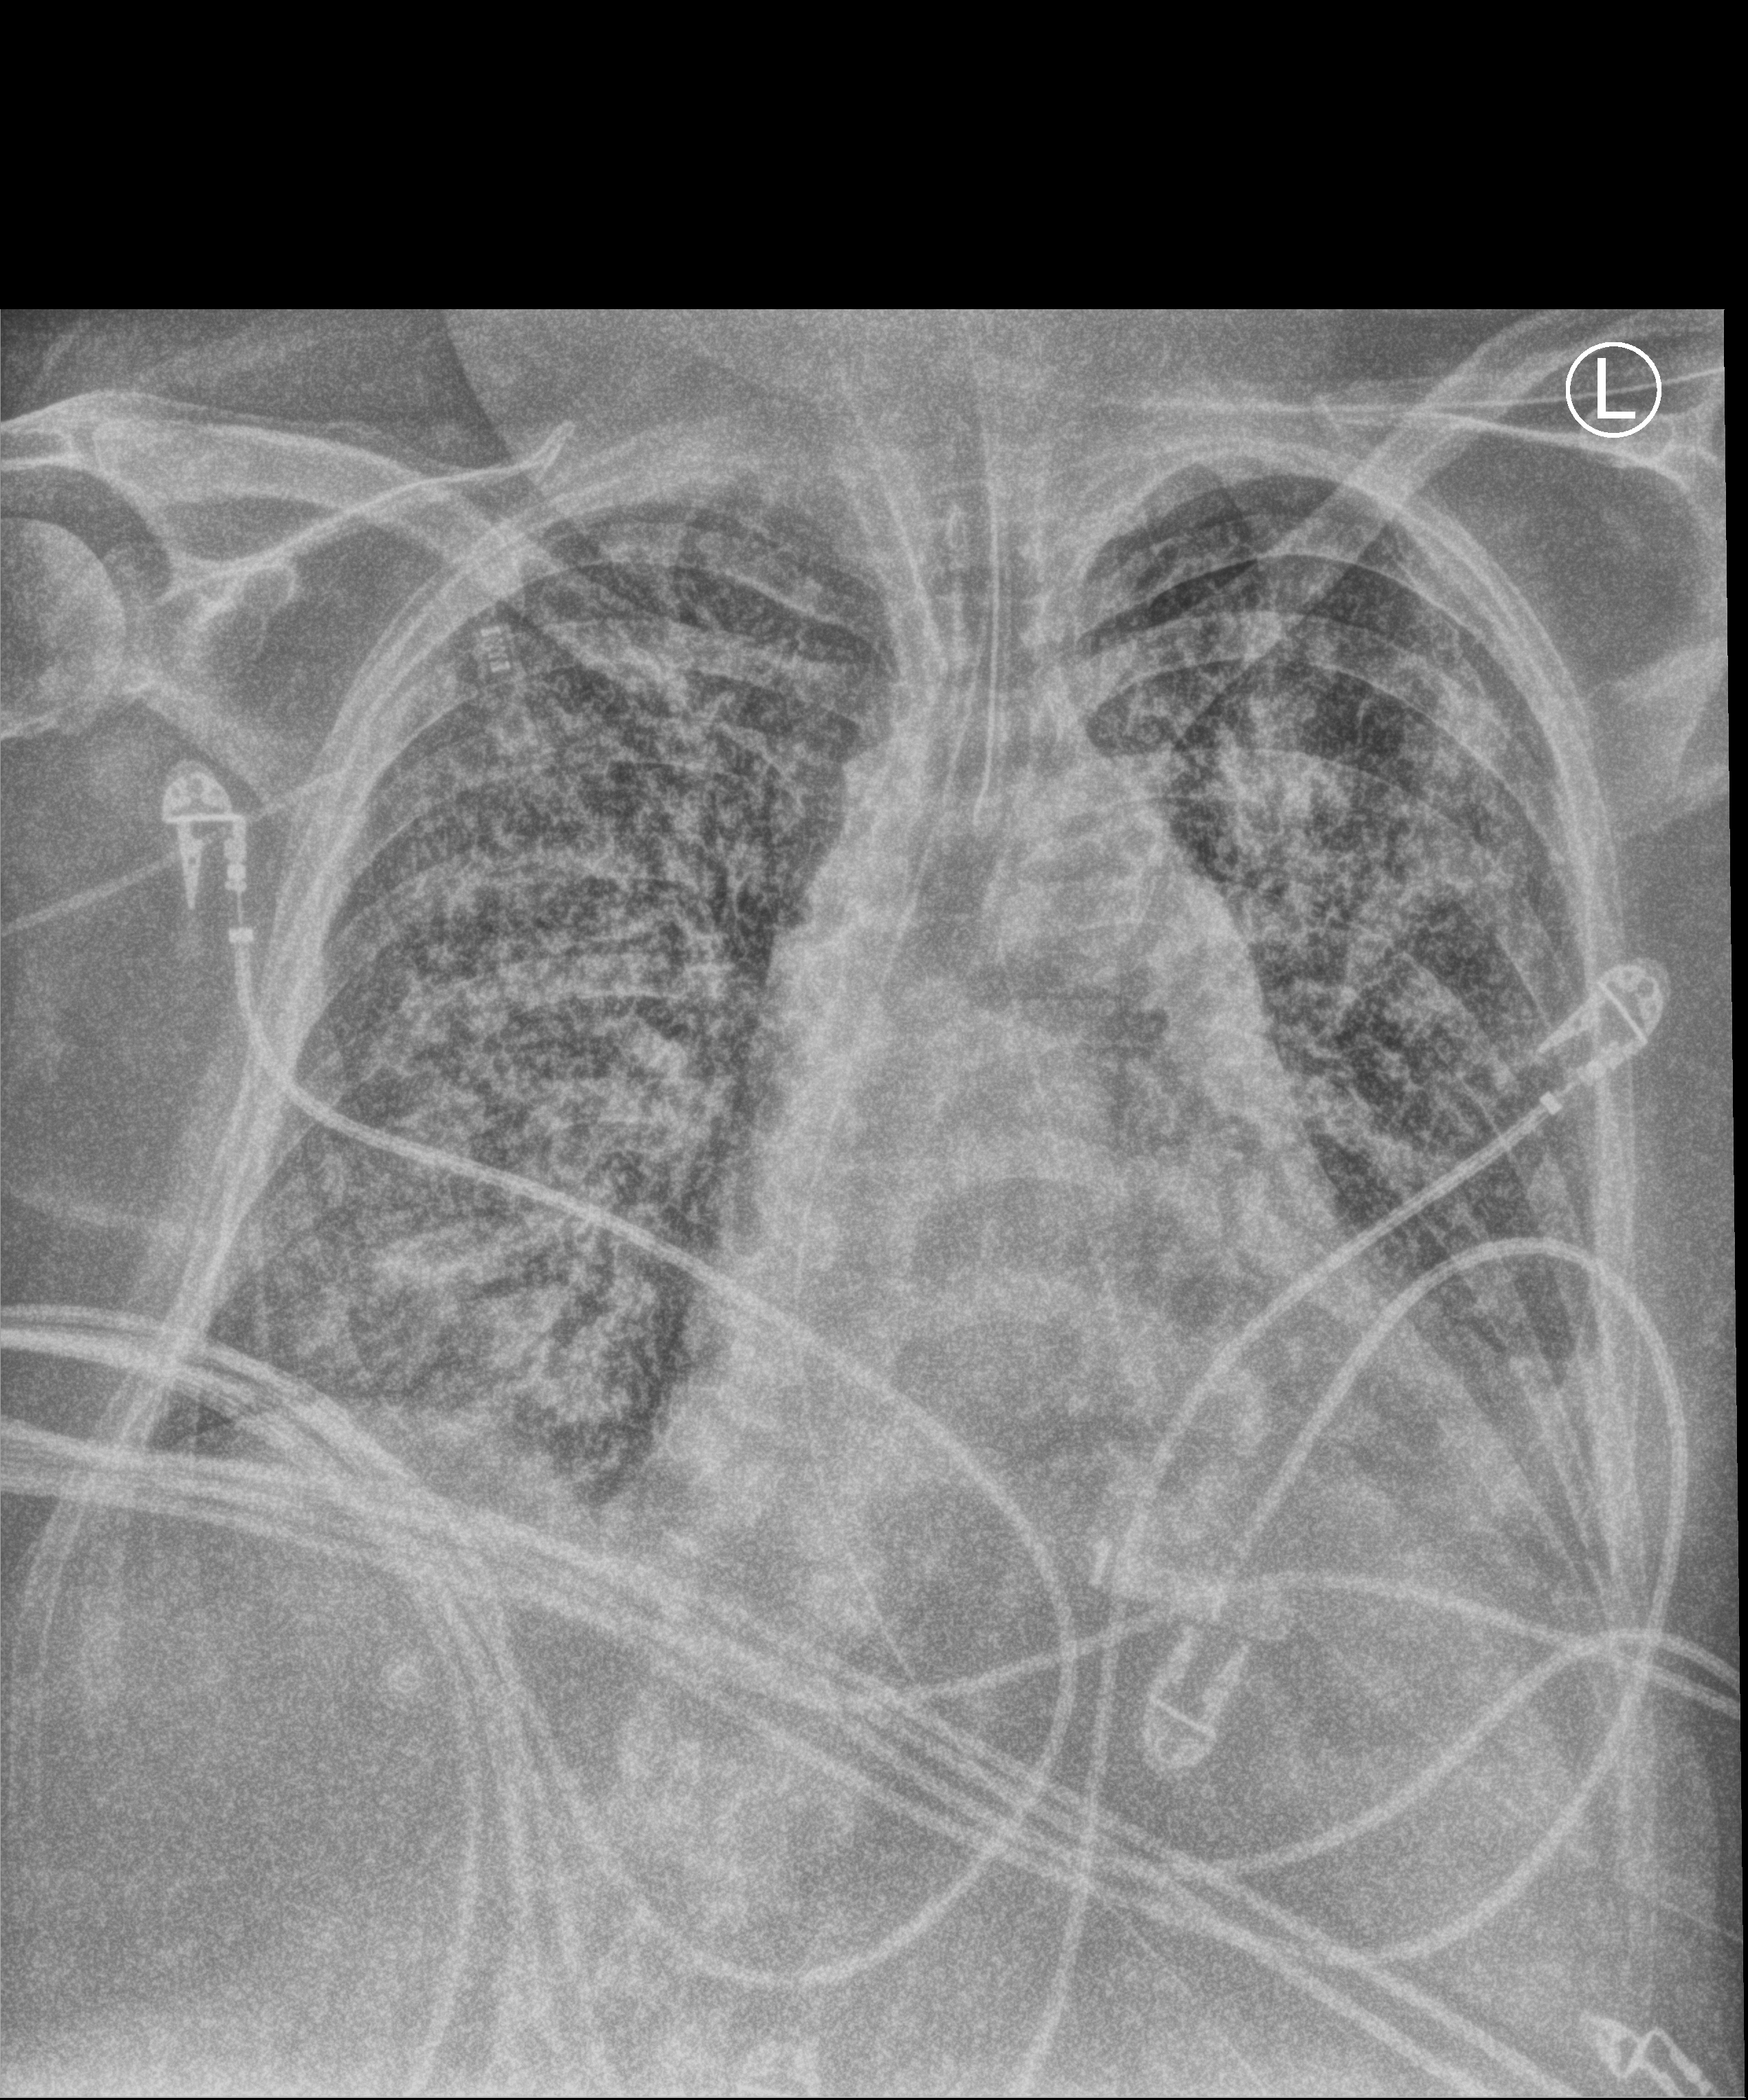
Bedside chest radiograph (computed radiography); anteroposterior (AP) projection. Female patient hospitalised with COVID-19, age 60–74 years.
Admission-level facts for this patient (not findings on this image; timing relative to this image not recorded): COPD (admission record): no; admitted to intensive care during this hospital stay: yes.